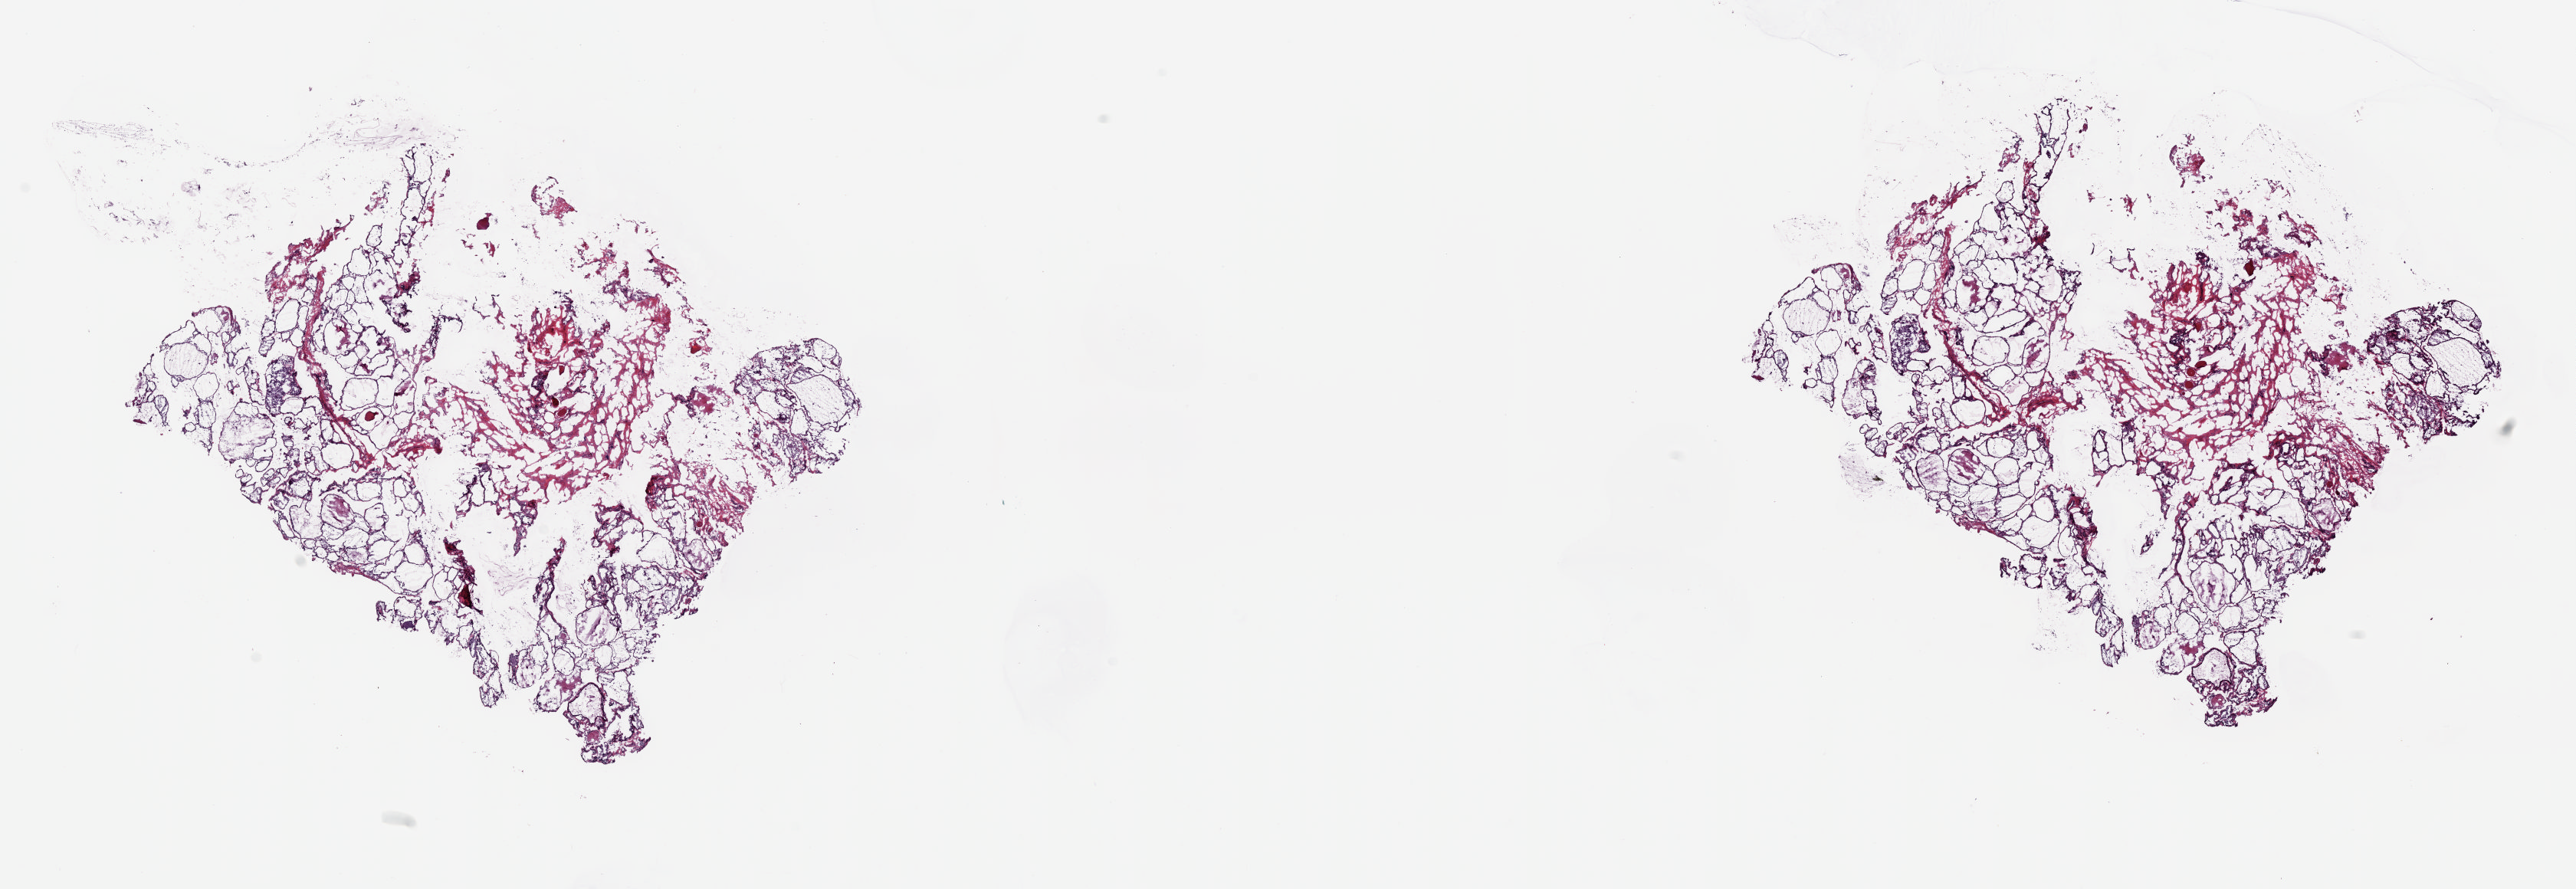
Digitized Hematoxylin and eosin (H&E) stained tissue section (whole slide) — whole scanned area (about 26.6 x 9.2 mm) shown as a low-resolution overview, frozen section from the top of the tissue portion, solid tissue normal (non-tumour tissue) sample from the thyroid. Patient: male, age at initial diagnosis 42 years. Composition of this section per pathologist review: tumour cells 0%, tumour nuclei 0%, normal cells 100%, stromal cells 0%, necrosis 0%. Inflammatory infiltration, as recorded: lymphocyte infiltration 1%, monocyte infiltration 53%, neutrophil infiltration 0%.
* this section: solid tissue normal sample (biorepository sample class)
* patient diagnosis: Papillary adenocarcinoma, NOS (thyroid gland)